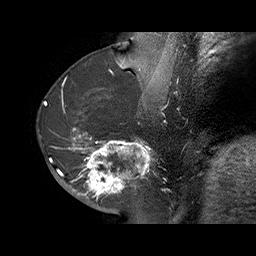
Breast MRI (dynamic contrast-enhanced), one sagittal slice; position 28 of 70 along the scan axis; dynamic contrast-enhanced series, time point 2 of 6 at this slice position (early post-contrast); 1.5 T; TE 4.5 ms, TR 32.4 ms; 3 mm slice thickness; 256 × 256 image matrix. Female patient. Case-level facts recorded for this patient, not image findings: setting: breast cancer imaged before/during neoadjuvant chemotherapy; receptor status: HR-positive, HER2-negative.
Structures marked on this image (semi-automatically segmented with operator editing):
- analysis volume of interest (the breast-tissue region the enhancement analysis was run in; not a lesion): bounding box [x1, y1, x2, y2] px = [71, 128, 159, 202]
- tumour enhancement mask (voxels above the 100 % enhancement threshold inside the analysis volume of interest): [71, 128, 150, 200]